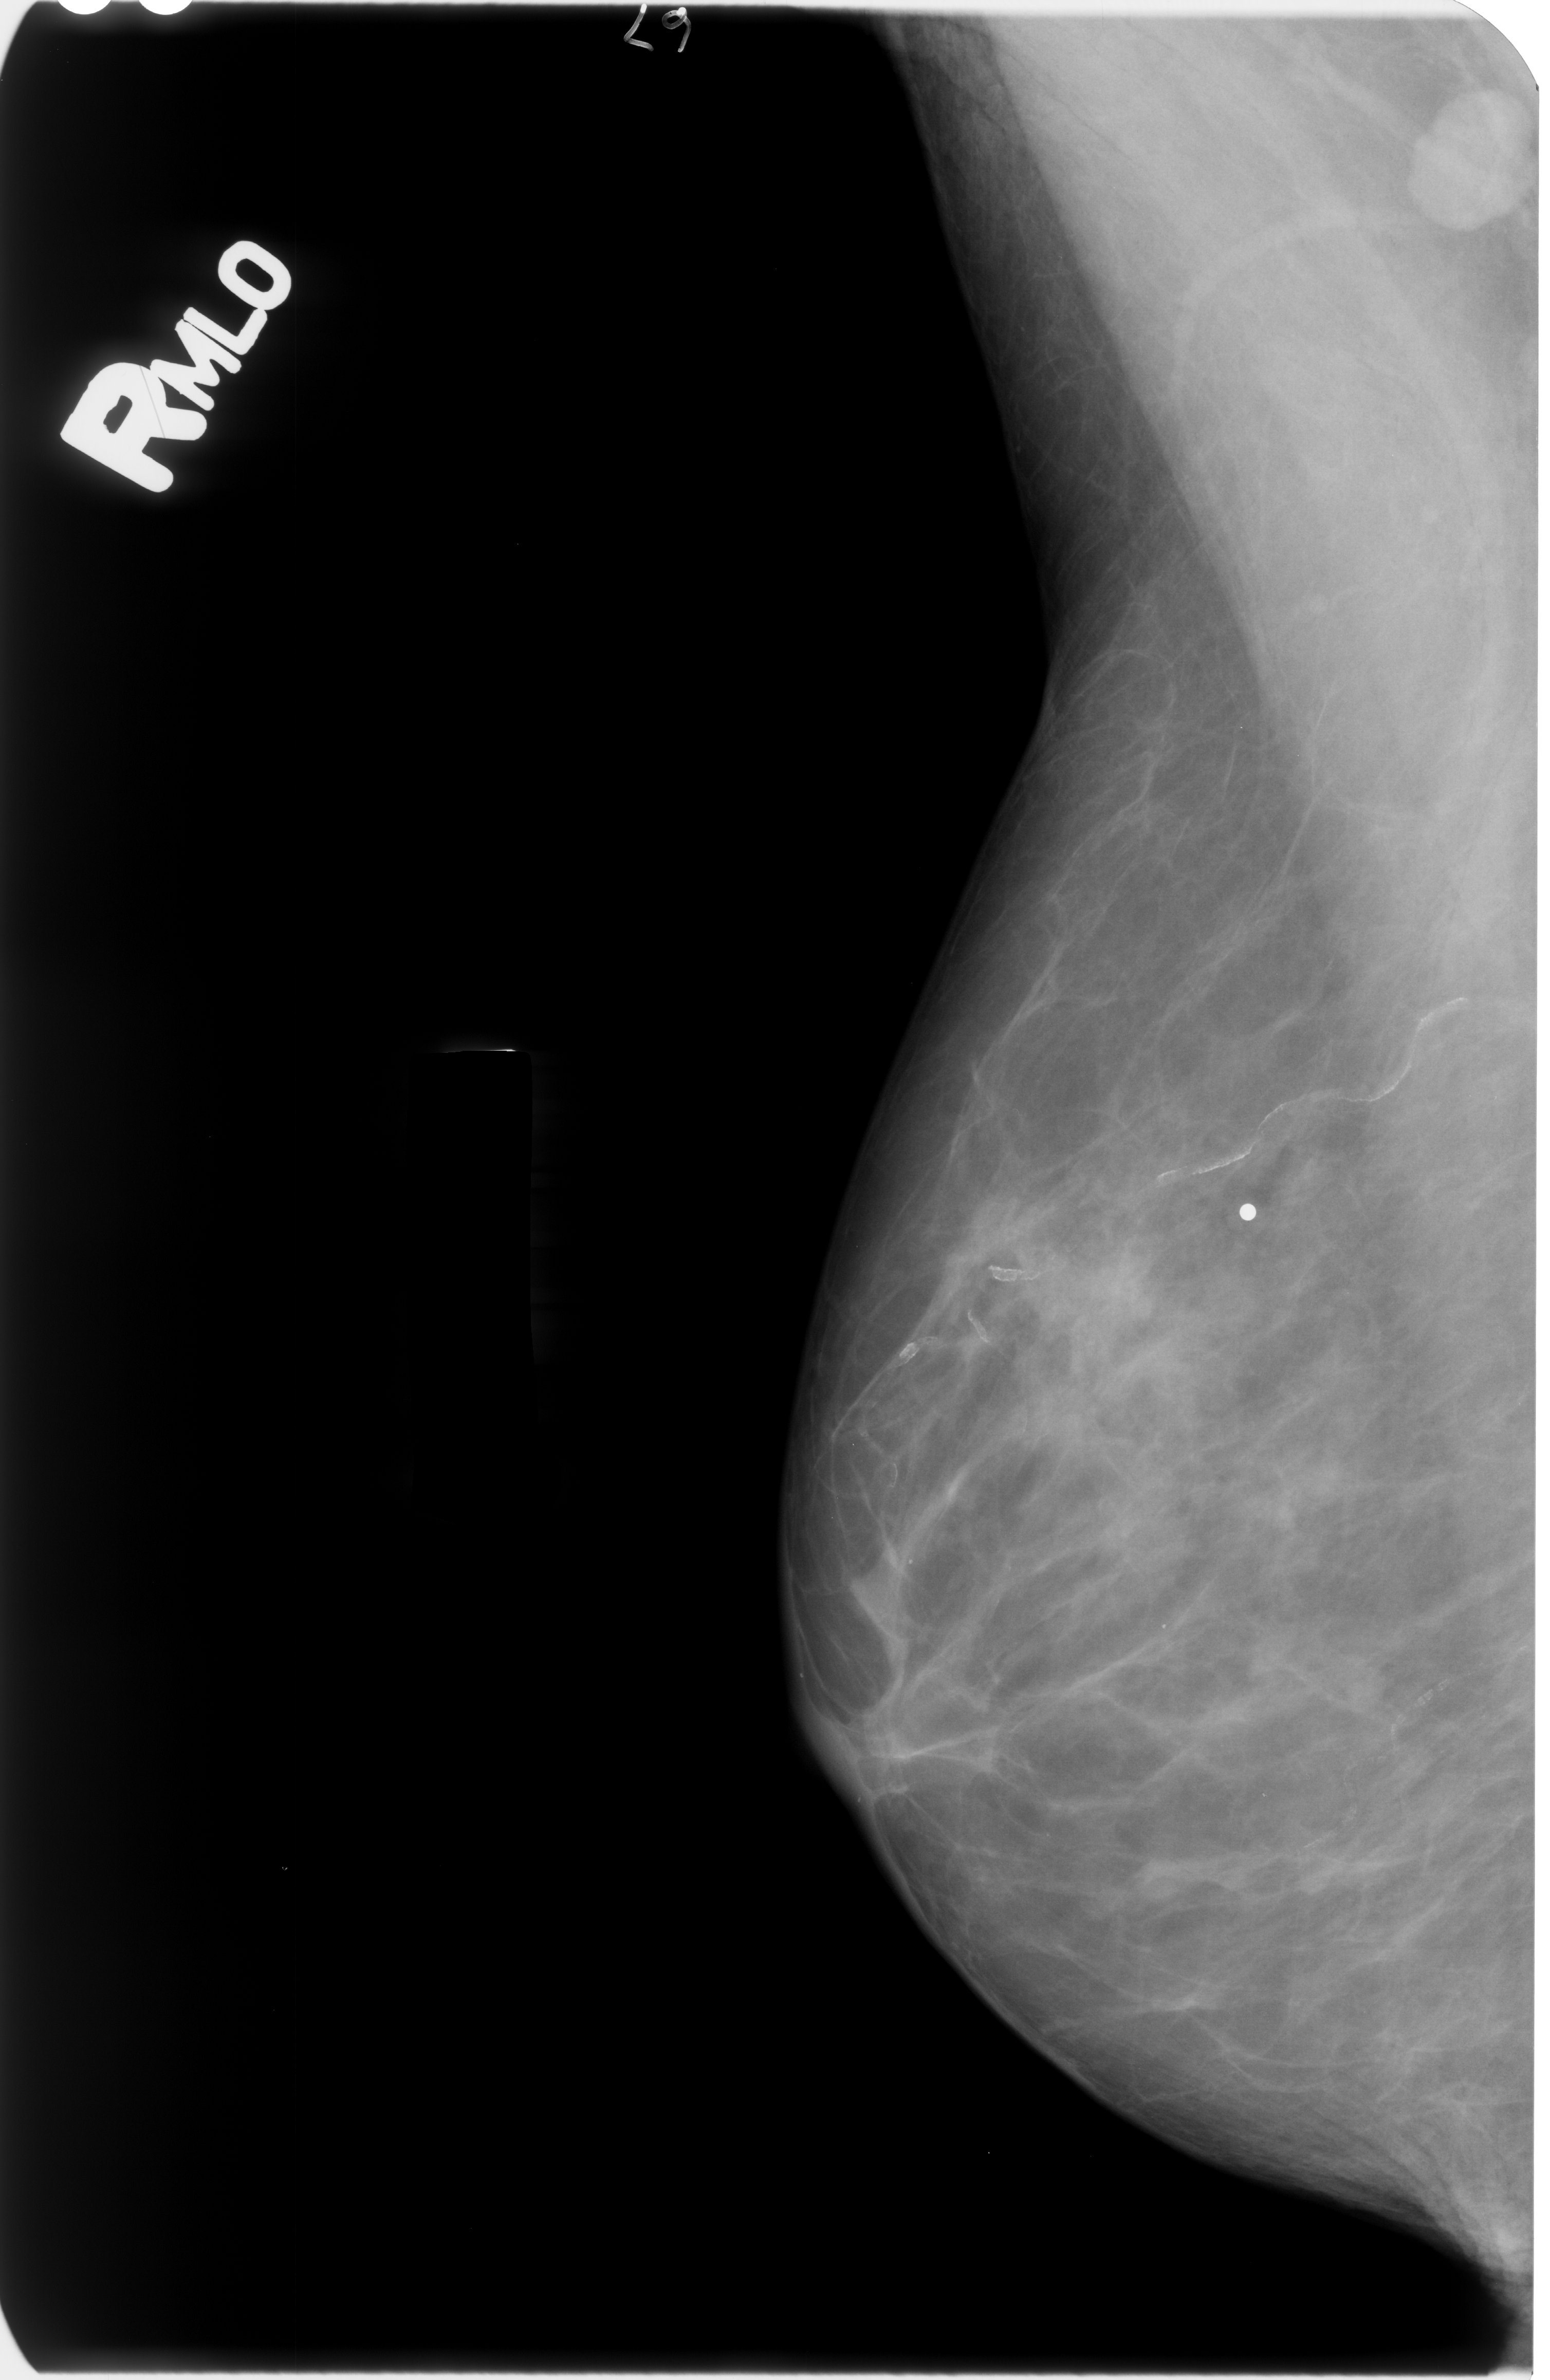
Mammogram (digitized film), right breast, mediolateral oblique (MLO) view, BI-RADS breast density category 2 (scale 1–4).
- Finding: calcifications, morphology vascular; BI-RADS assessment category 2; benign without callback (not worked up further).